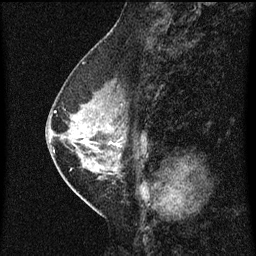
Breast MRI (dynamic contrast-enhanced), one sagittal slice. Slice 28 of 60 in the series (ordered by position). Dynamic contrast-enhanced series, image 2 of 3 at this slice position (ordered by acquisition). 1.5 T. TE 4.2 ms, TR 8 ms. 2 mm slice thickness. 256 × 256 image matrix. Patient: female, 47 years.
Structures marked on this image (semi-automatically segmented with operator editing):
- analysis volume of interest (the breast-tissue region the enhancement analysis was run in; not a lesion): bounding box [x1, y1, x2, y2] px = [54, 80, 143, 187]
- tumour enhancement mask (voxels above the 70 % enhancement threshold inside the analysis volume of interest): [55, 112, 121, 157]